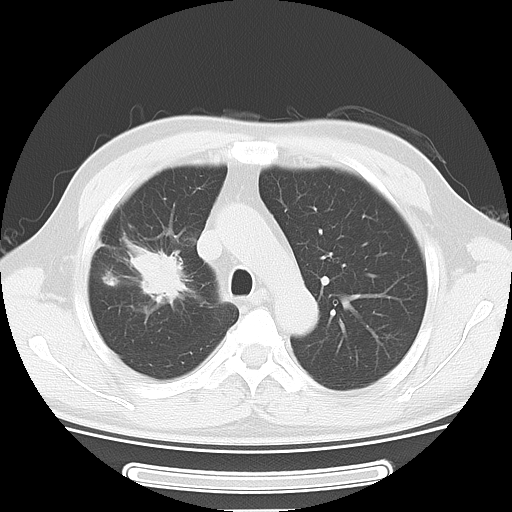
Chest CT, one axial slice. Position 38 of 51 along the scan axis. Lung window (W 1500 / L -600 HU). 5 mm slice thickness. 512 × 512 image matrix. Male patient, age 46 years. From the clinical record (not read from this slice): clinical TNM (as recorded): T3 N0 M1b.
Annotated regions visible in this slice (rectangle marked by the reading radiologist):
- lung tumour (recorded histology: adenocarcinoma): box from (x=114, y=227) to (x=189, y=315) px